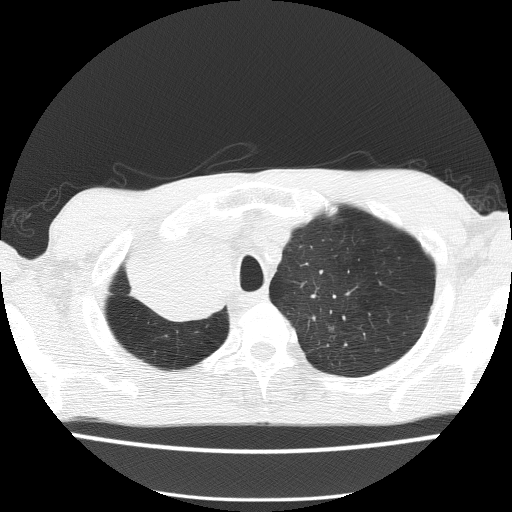
Low-dose screening chest CT, one axial slice. 120 kVp. Lung window (W 1500 / L -600 HU). 2 mm slice thickness. 512 × 512 image matrix, field of view 336 × 336 mm.
Annotated regions visible in this slice (outlined manually by an expert reader):
- lesion 1 (tumor, hilum of right lung): bounding box (x1, y1, x2, y2) in pixels: (129, 233, 231, 319)